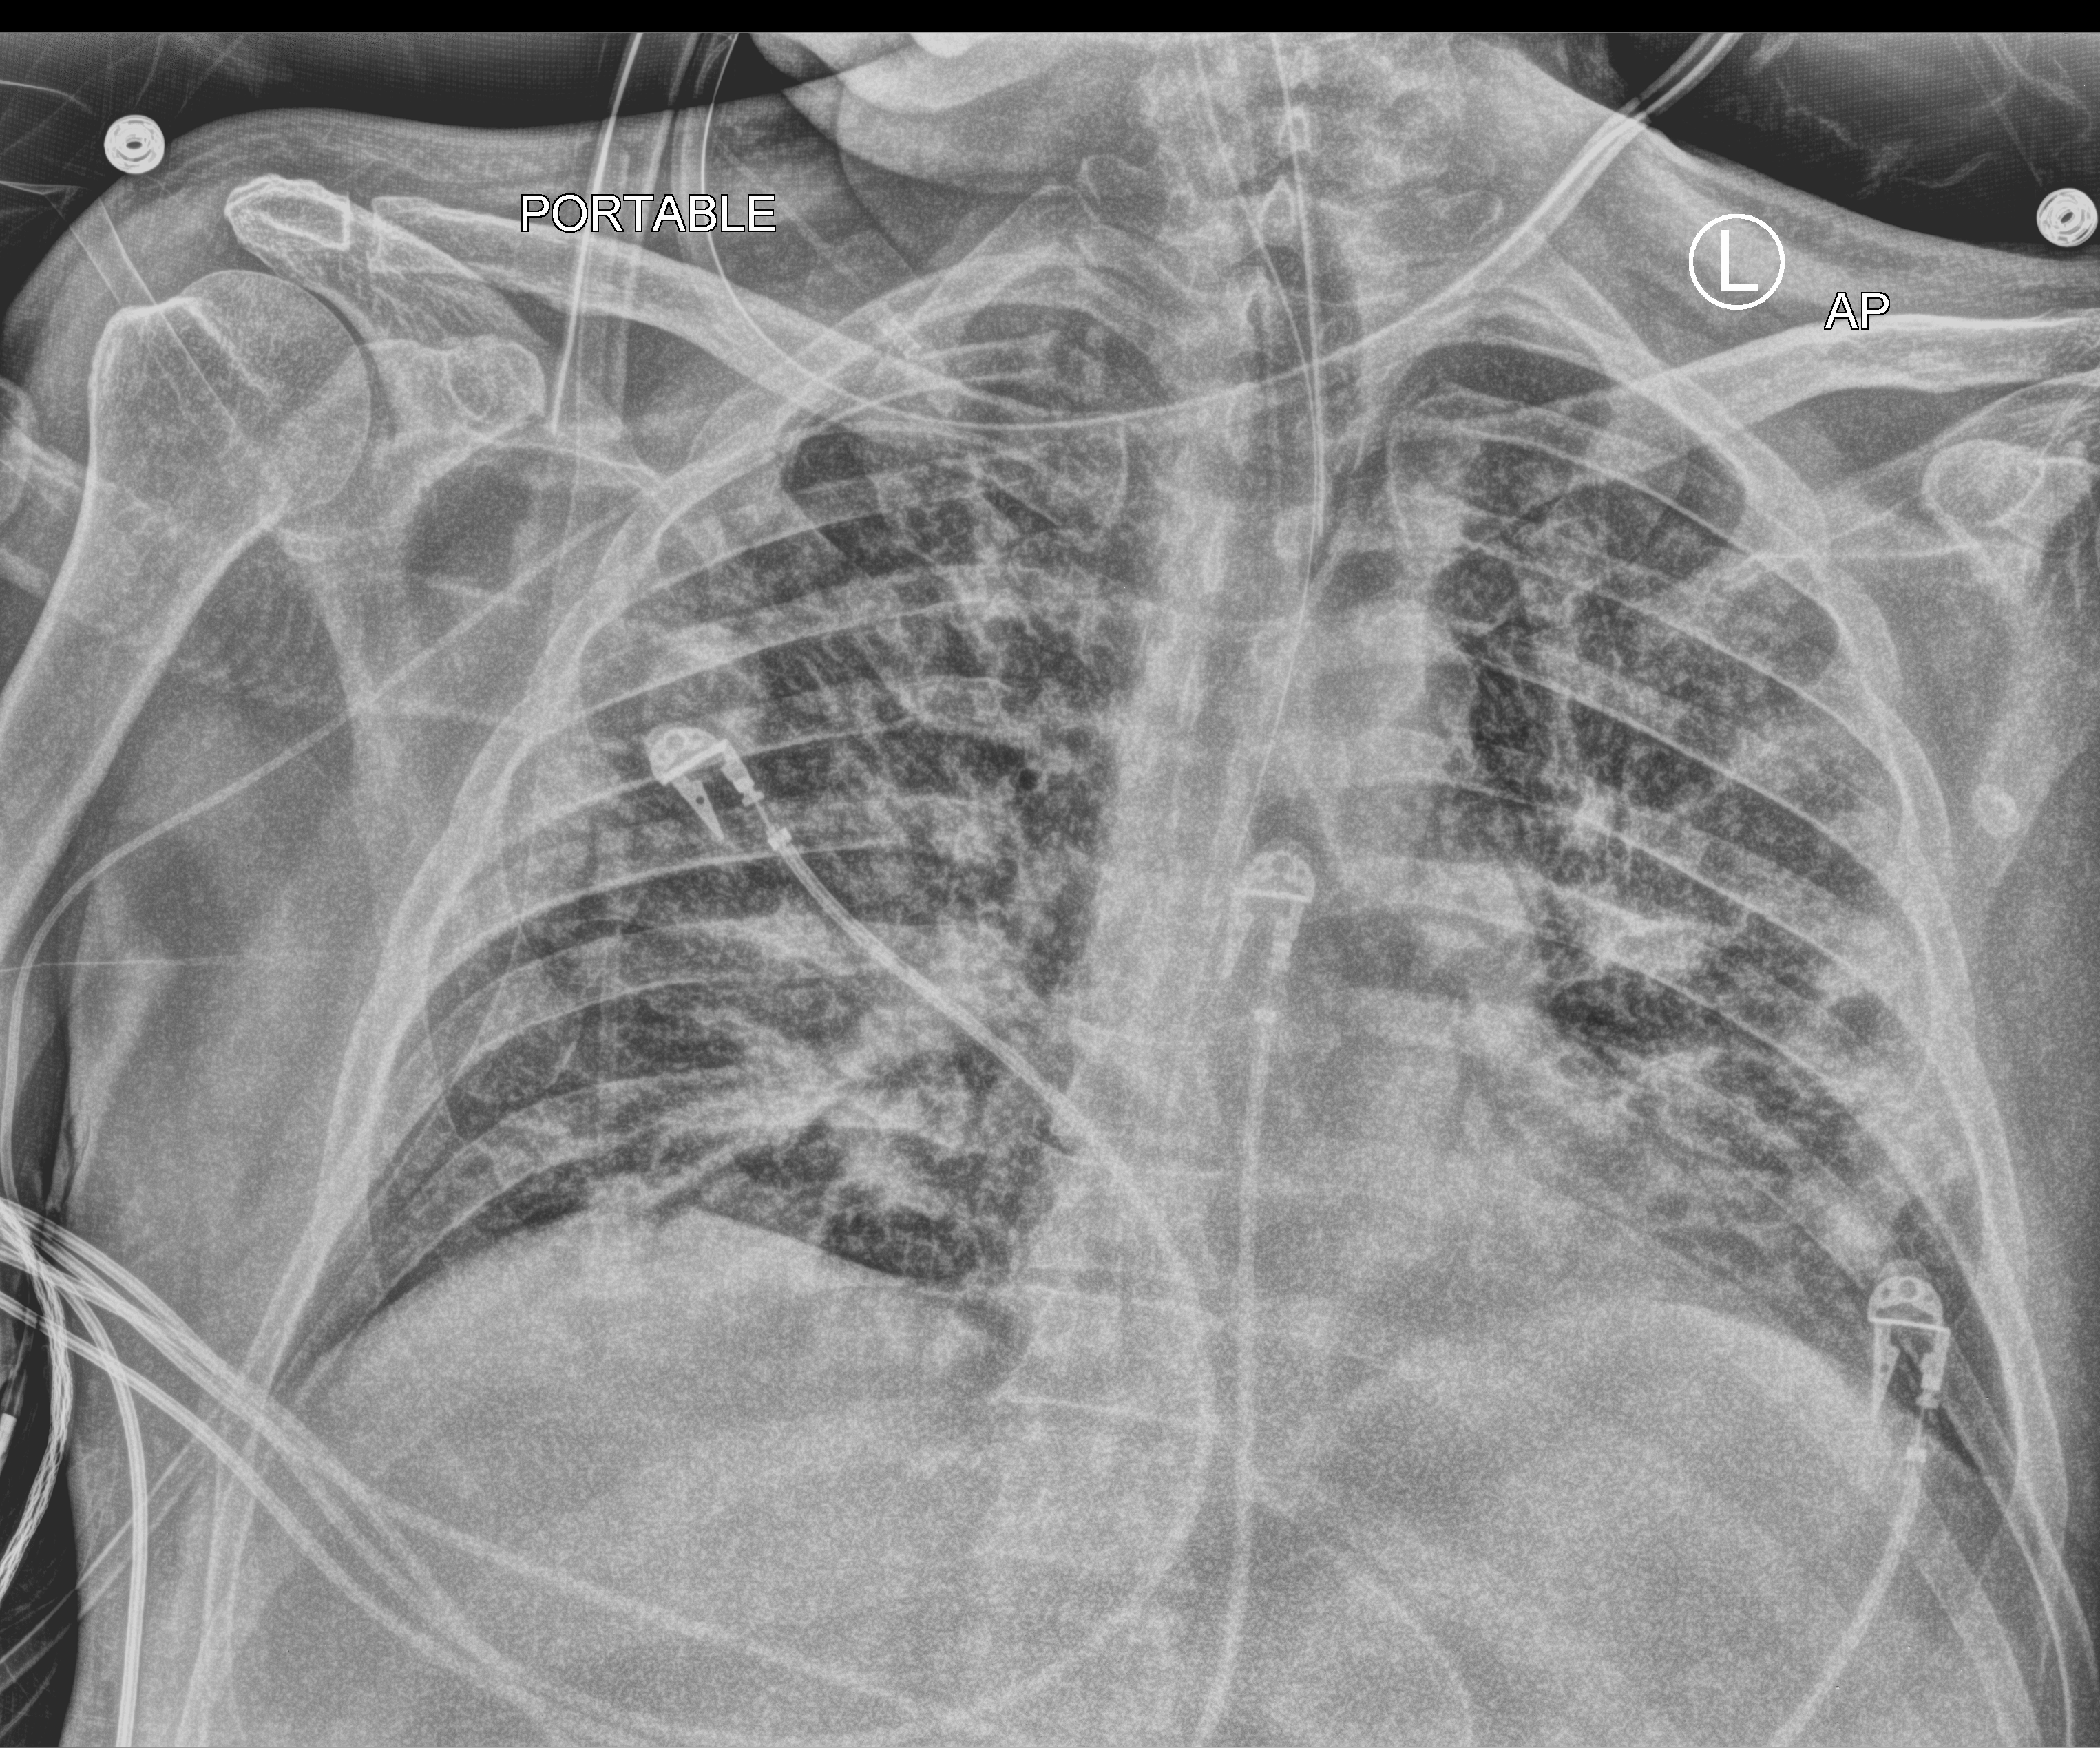
Chest X-ray (portable); anteroposterior (AP) projection. Patient hospitalised with COVID-19; male, aged 60–74 years.
Admission-level facts for this patient (not findings on this image; timing relative to this image not recorded): mechanically ventilated during this hospital stay: yes.